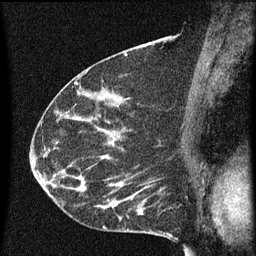
Breast MRI (dynamic contrast-enhanced), one sagittal slice; slice 36 of 60 in the series (ordered by position); dynamic contrast-enhanced series, image 2 of 3 at this slice position (ordered by acquisition); 1.5 T; TE 4.2 ms, TR 8 ms; 256 × 256 image matrix, field of view 180 × 180 mm. Patient: female, 55 years.
Outlined on this slice (semi-automatic segmentation, software-assisted and operator-edited):
- analysis volume of interest (the breast-tissue region the enhancement analysis was run in; not a lesion): box from (x=51, y=156) to (x=145, y=217) px
- tumour enhancement mask (voxels above the 70 % enhancement threshold inside the analysis volume of interest): (x=53, y=156)–(x=143, y=215)